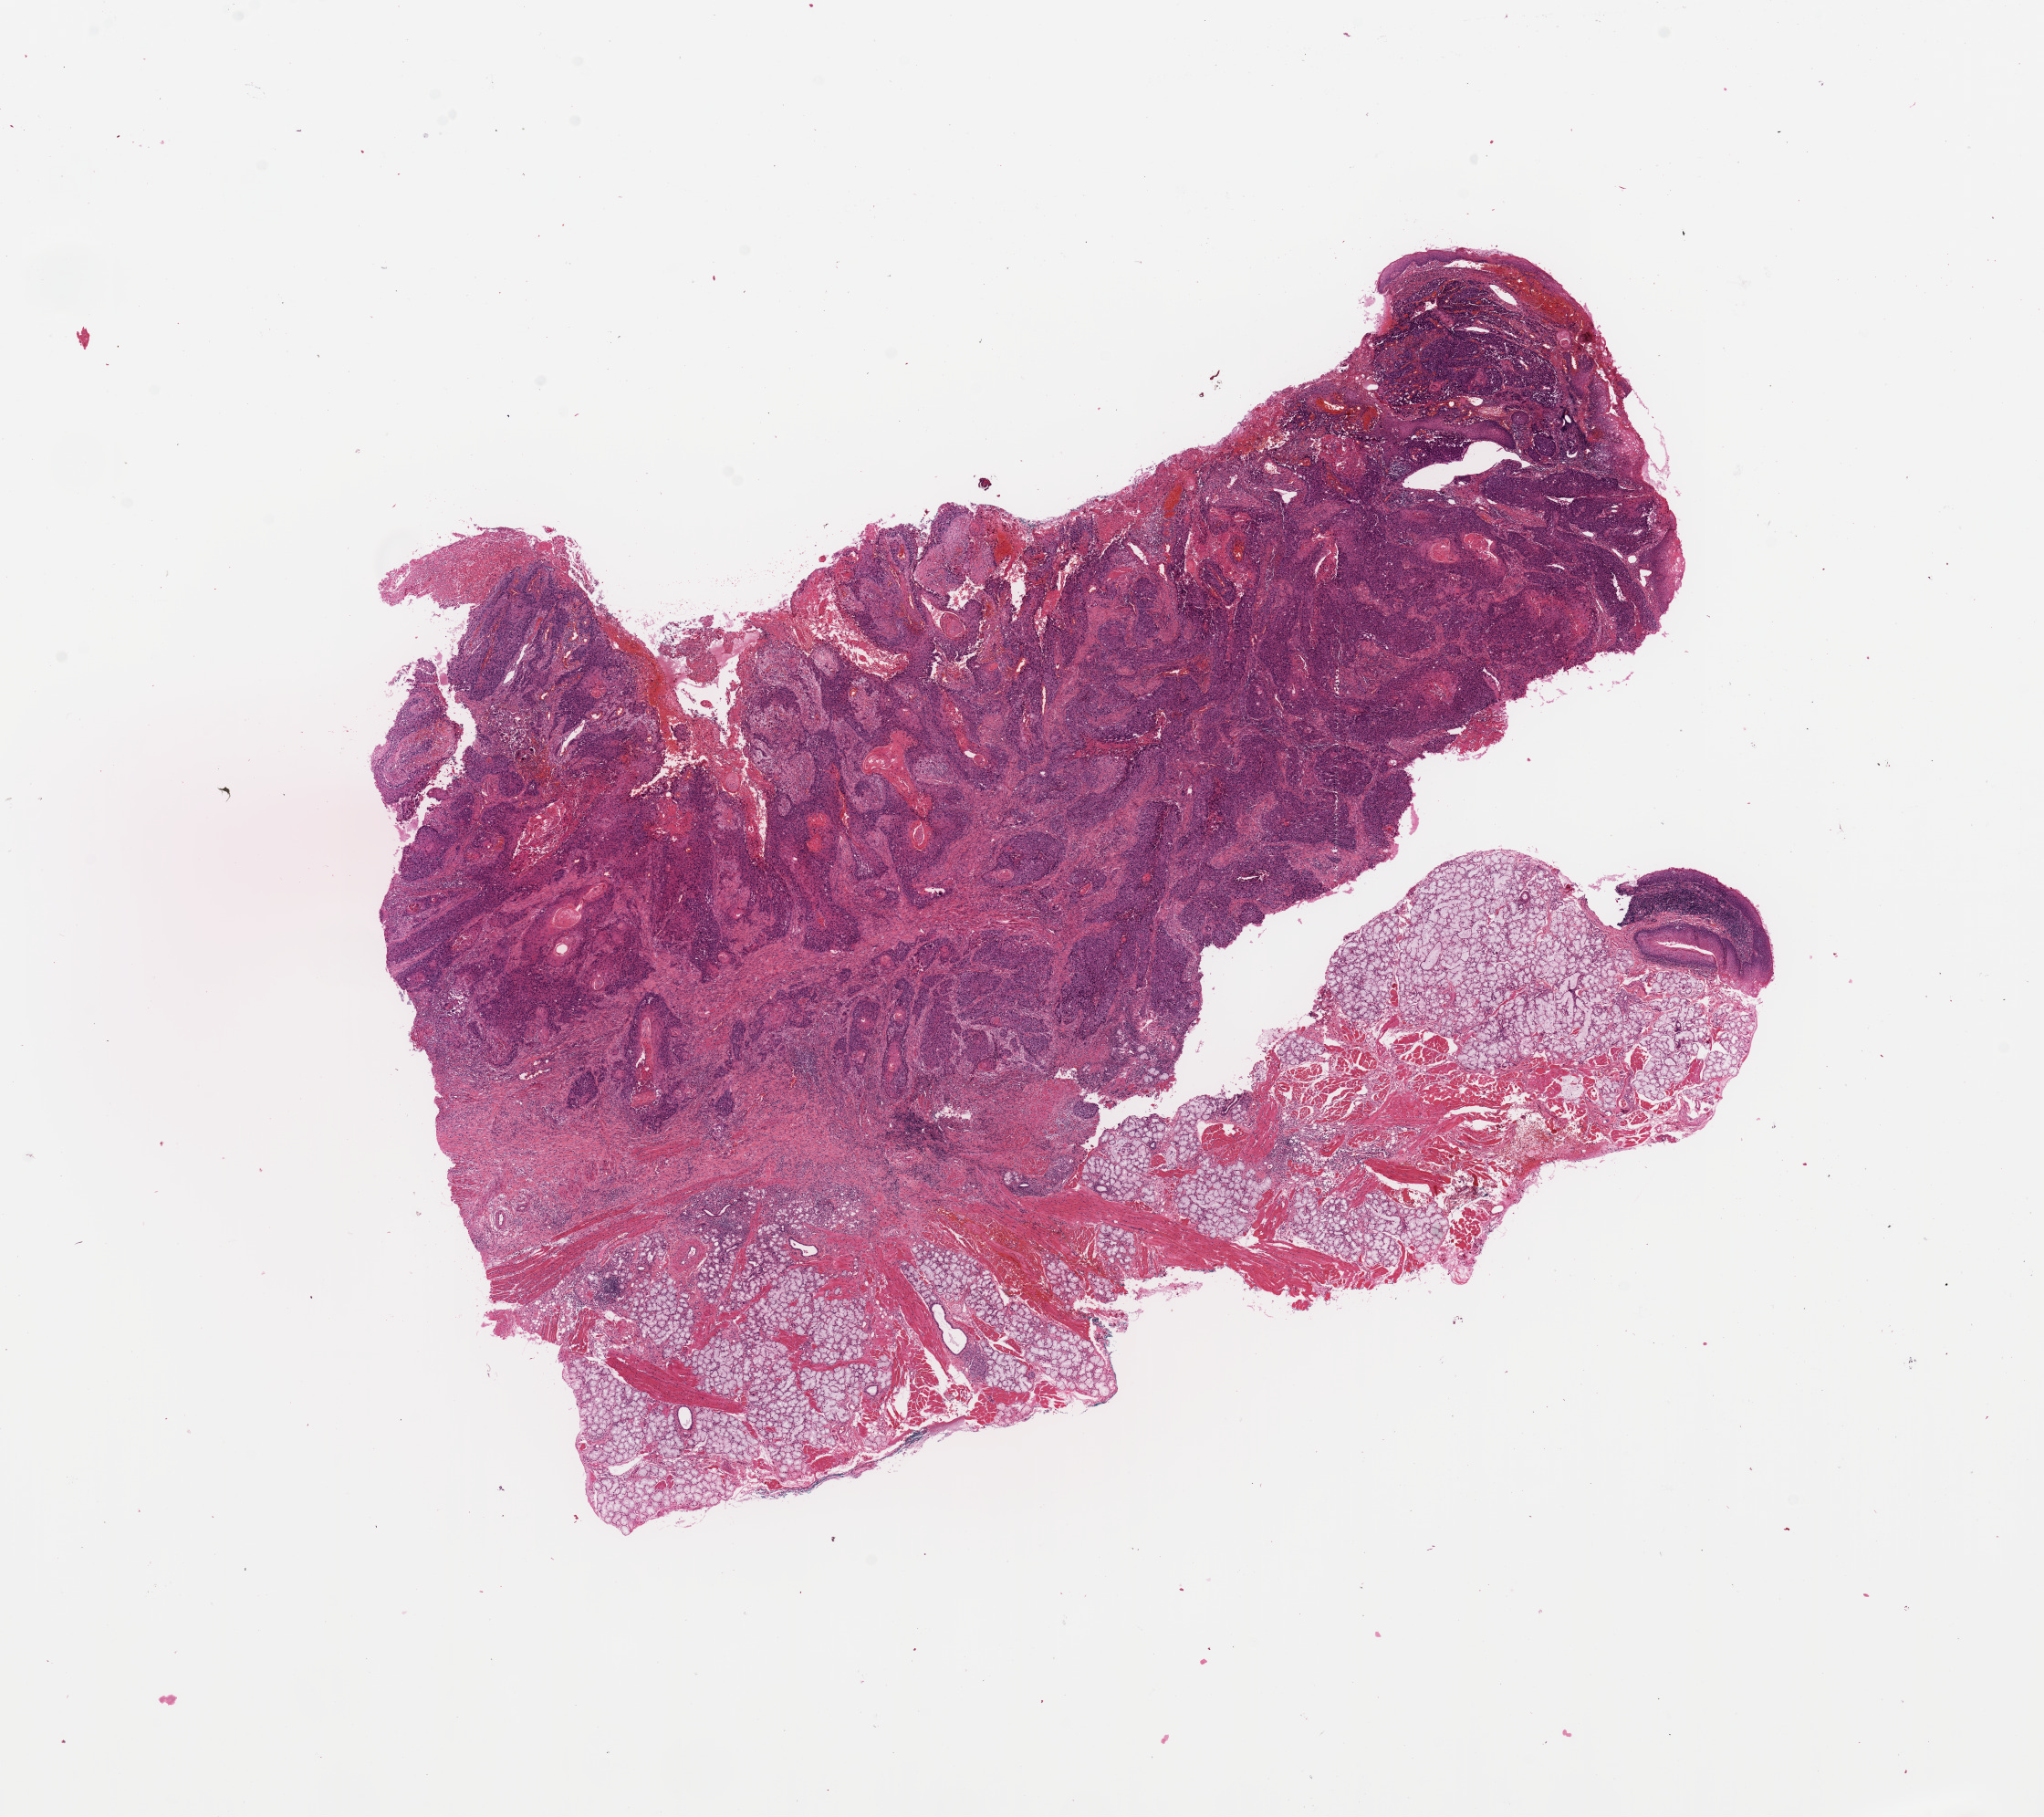
H&E whole-slide image — whole scanned area (about 17.7 x 15.7 mm) shown as a low-resolution overview. Head and neck, tissue type not recorded. 47-year-old male patient.
• patient diagnosis: Squamous cell carcinoma, NOS (oropharynx, NOS)